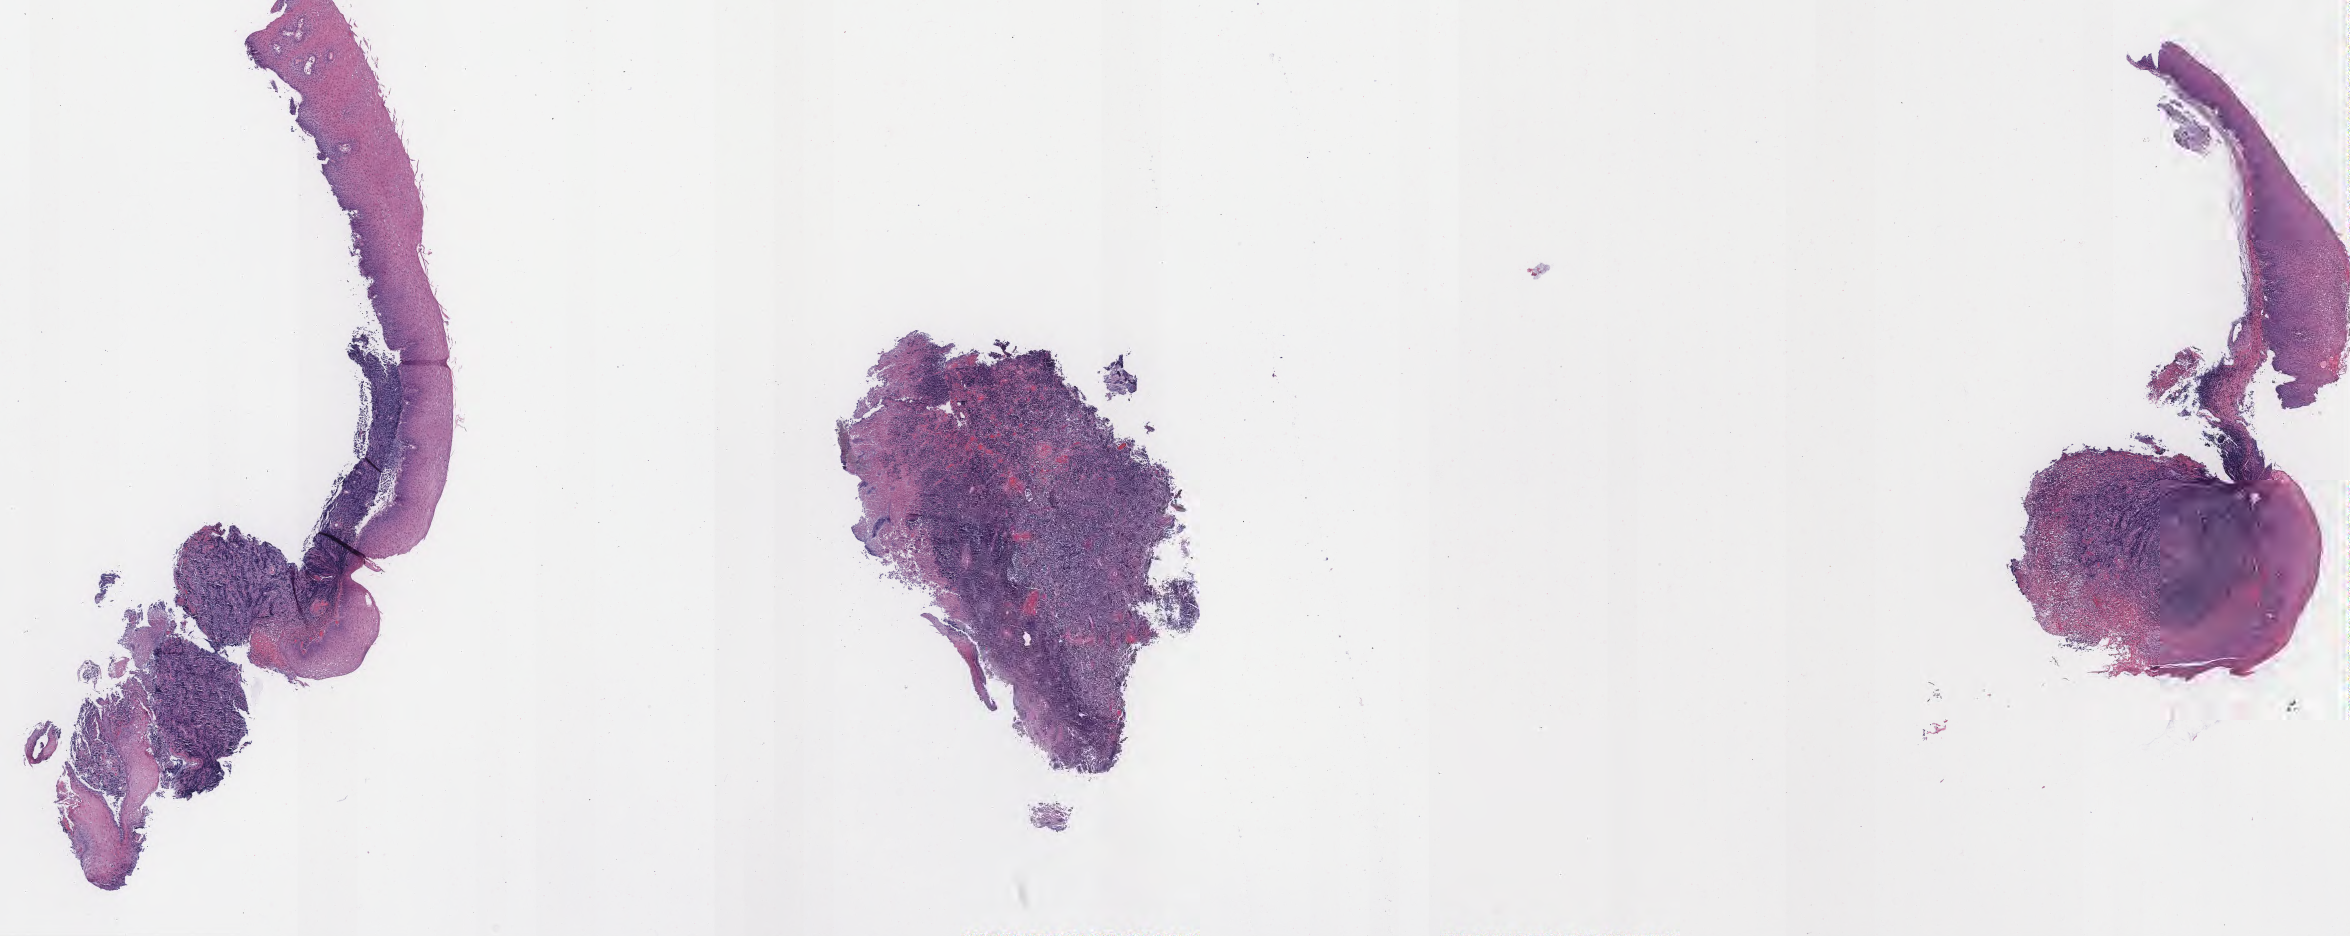
Digitized haematoxylin and eosin-stained section — low-resolution overview of the scanned area, about 18.7 x 7.4 mm. Formalin-fixed, paraffin-embedded (FFPE) tissue. Specimen: primary tumor. Patient male; 66 years old. Slide review estimates, as recorded: tumor cells 50%, tumor nuclei 70%, stromal cells 10%, necrosis 30%, normal cells 10%. Infiltration values recorded for this section: lymphocyte infiltration 50%, monocyte infiltration 20%, neutrophil infiltration 10%.
Ann Arbor stage (patient): Stage III. Diagnosis: Burkitt lymphoma, NOS.